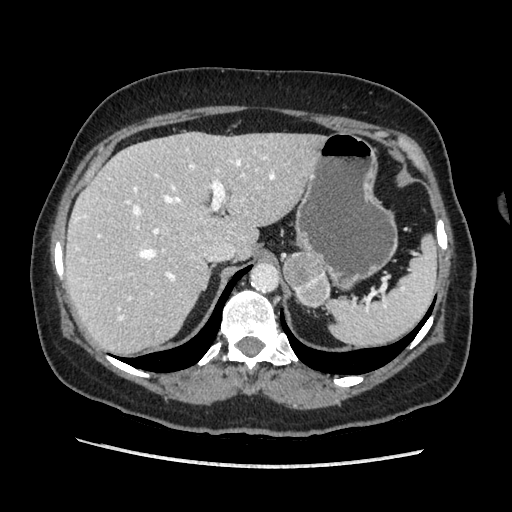
Contrast-enhanced abdominal CT, one axial slice. Soft-tissue window (W 400 / L 40 HU). 1.25 mm slice thickness. 512 × 512 image matrix, field of view 360 × 360 mm. Female patient. Case-level facts recorded for this patient, not image findings: diagnosis: adrenocortical carcinoma; tumour side: left adrenal; tumour size at pathology: 6.5 cm; Ki-67 index: 22 %; stage (as recorded): 2.
Structures marked on this image (semi-automatic segmentation, software-assisted and operator-edited):
- mass: box from (x=283, y=253) to (x=330, y=306) px